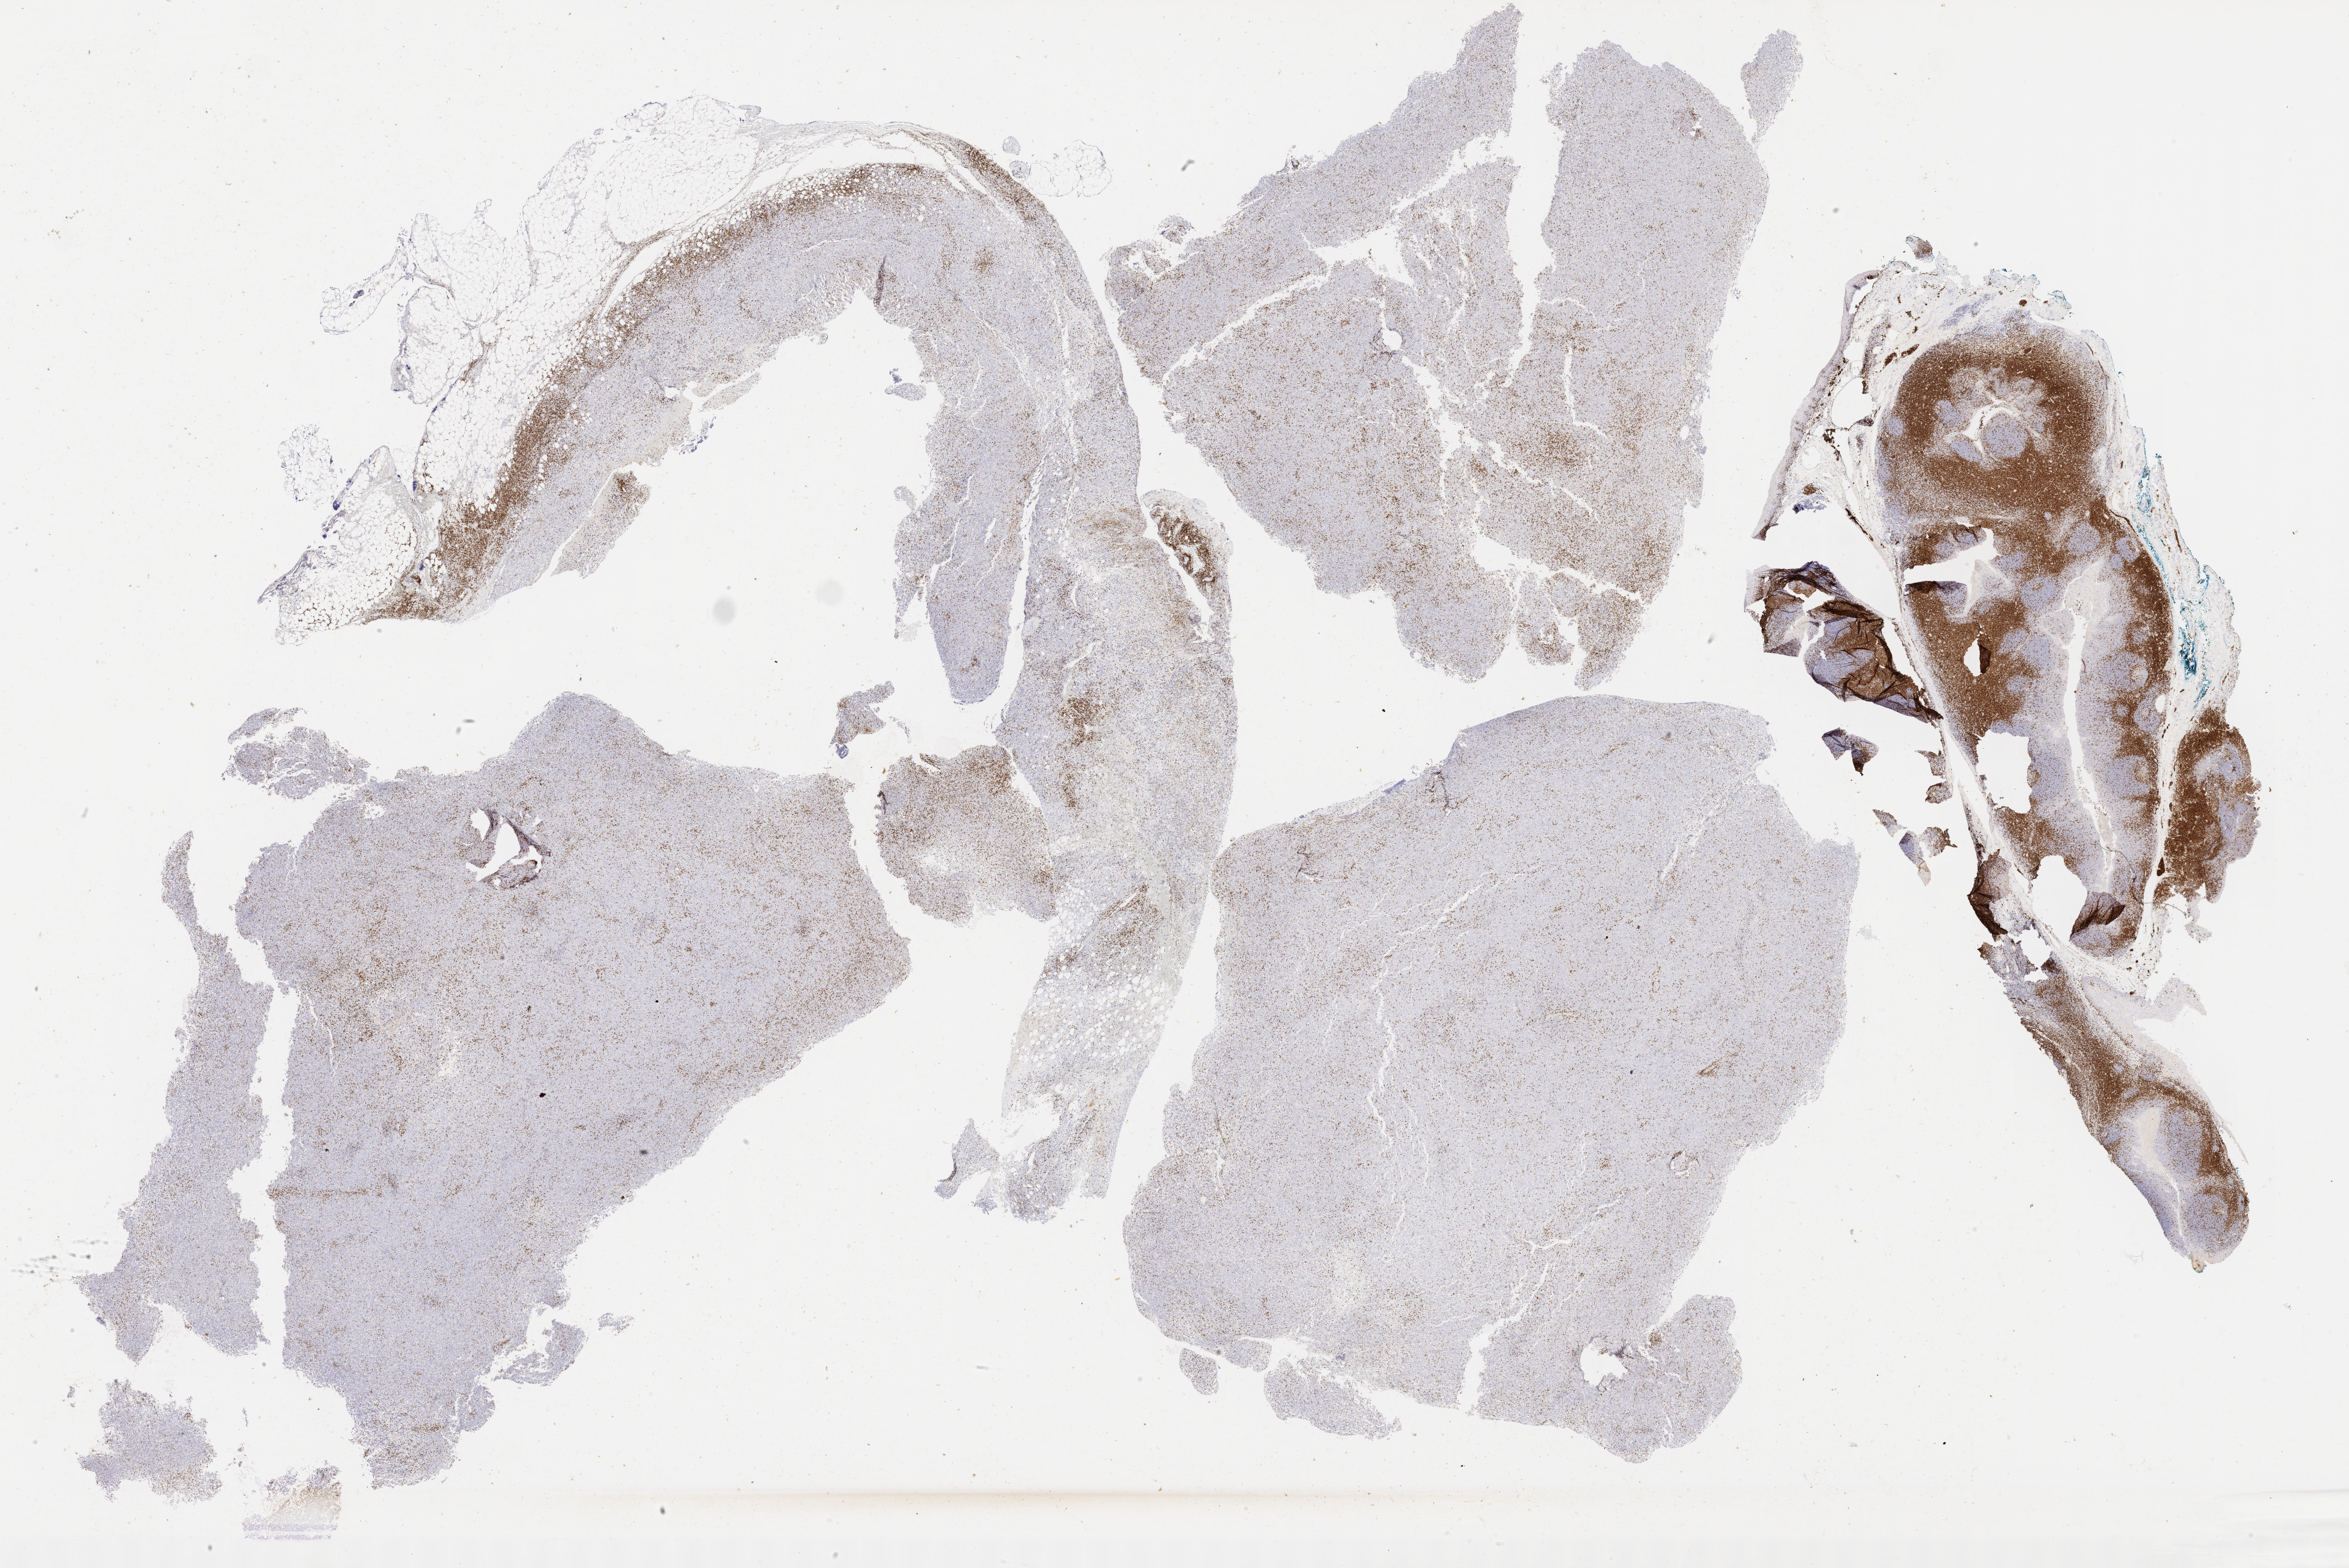
Whole-slide image, immunohistochemical stain for CD3, whole scanned area (about 31.7 x 21.2 mm) shown as a low-resolution overview. Female patient.
Specimen: tumor tissue.